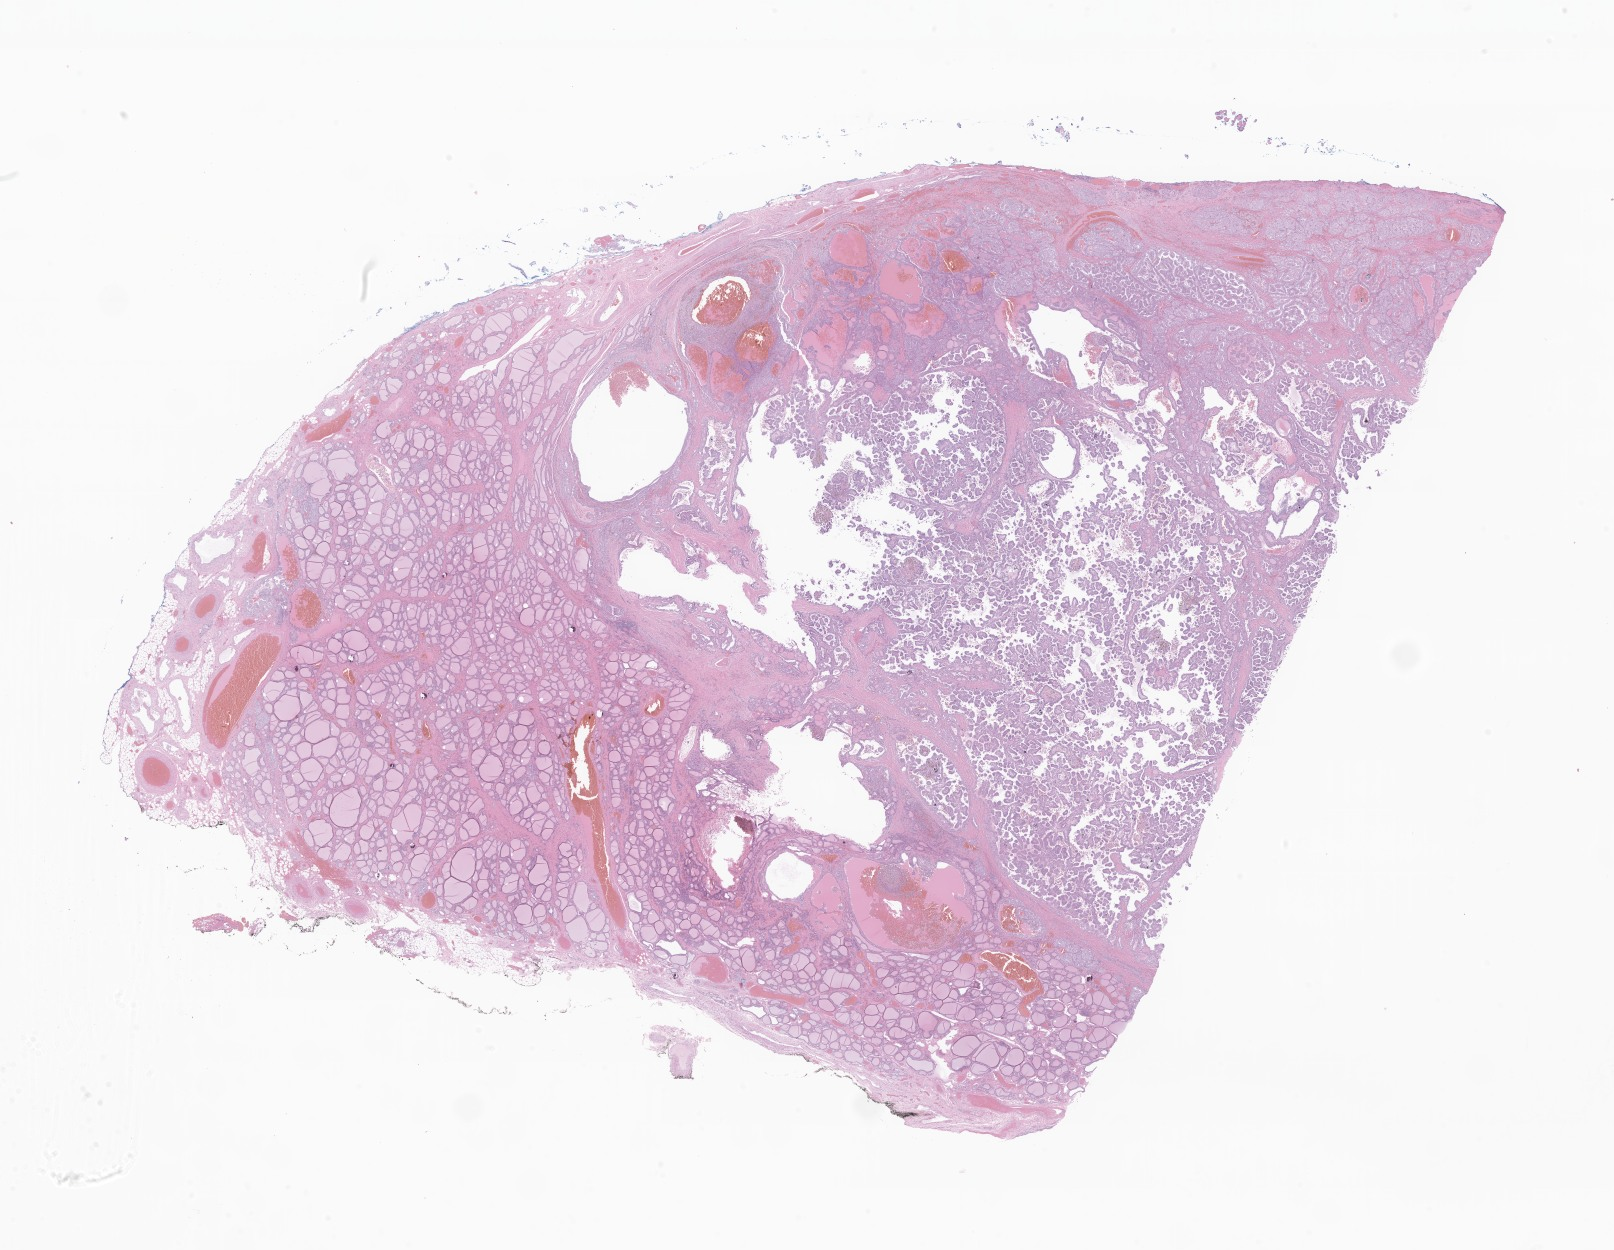
Digitized hematoxylin and eosin (H&E)-stained section of tumor tissue from the thyroid — low-resolution overview of the scanned area, about 27.2 x 21.1 mm, FFPE section. Patient: male, age 173 months (14 years 5 months).
• diagnosis: Neoplasm, uncertain whether benign or malignant